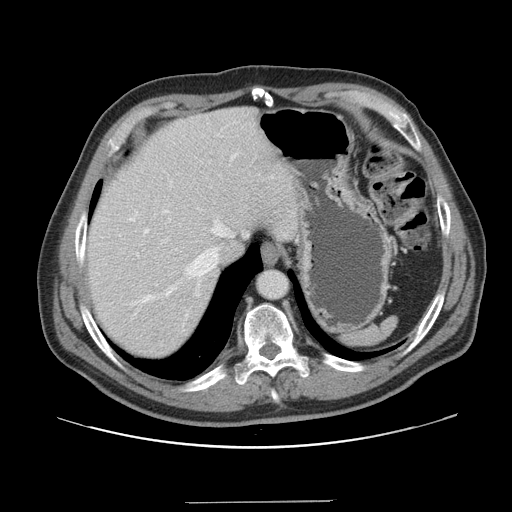
Contrast-enhanced abdominal CT, one axial slice. Slice 128 of 151 in the series (ordered by position). 120 kVp. Intravenous contrast given. Soft-tissue window (W 400 / L 40 HU). 2.5 mm slice thickness. 512 × 512 image matrix, field of view 399 × 399 mm. Male patient, age 63 years. Case-level facts recorded for this patient, not image findings: diagnosis: colorectal cancer liver metastases, imaged before liver resection; multiple liver metastases: no; largest metastasis: 2.1 cm; disease in both lobes: no.
Outlined on this slice (expert manual segmentation):
- hepatic veins: box from (x=129, y=155) to (x=235, y=302) px
- liver: (x=87, y=108)–(x=301, y=359)
- planned liver remnant (the part of the liver to remain after resection): (x=87, y=121)–(x=252, y=359)